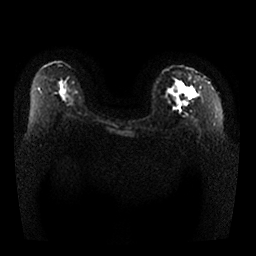
Breast MRI, one axial slice; diffusion-weighted series; image 2 of 4 stored at this slice position (different b-values; order by instance number); 1.5 T; 4 mm slice thickness; 256 × 256 image matrix, field of view 350 × 350 mm. Female patient.
Structures marked on this image (expert manual segmentation):
- tumour on diffusion-weighted imaging: box from (x=185, y=89) to (x=193, y=99) px